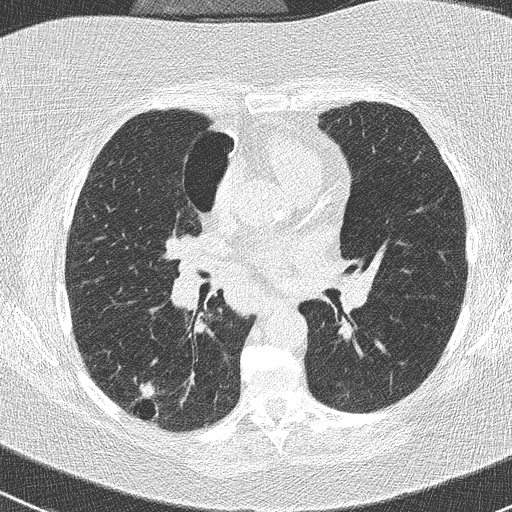
Chest CT (low-dose screening protocol), one axial image, baseline annual screen, lung window (W 1500 / L -600 HU), 120 kVp, slice 123 of 261 in the series. Female participant, aged 74 years at enrolment. Former smoker at enrolment.
• Lesion marked by an expert reader, bounding box [x1, y1, x2, y2] px = [121, 373, 175, 430].
• The screening reader recorded 3 non-calcified nodules or masses ≥4 mm on this exam; which of them this box marks is not recorded.
• Later outcome: lung cancer diagnosed 16 days after this screen — non-small cell carcinoma, right lower lobe, poorly differentiated (G3), stage IIIA (AJCC 6th edition), 28 mm at pathology.